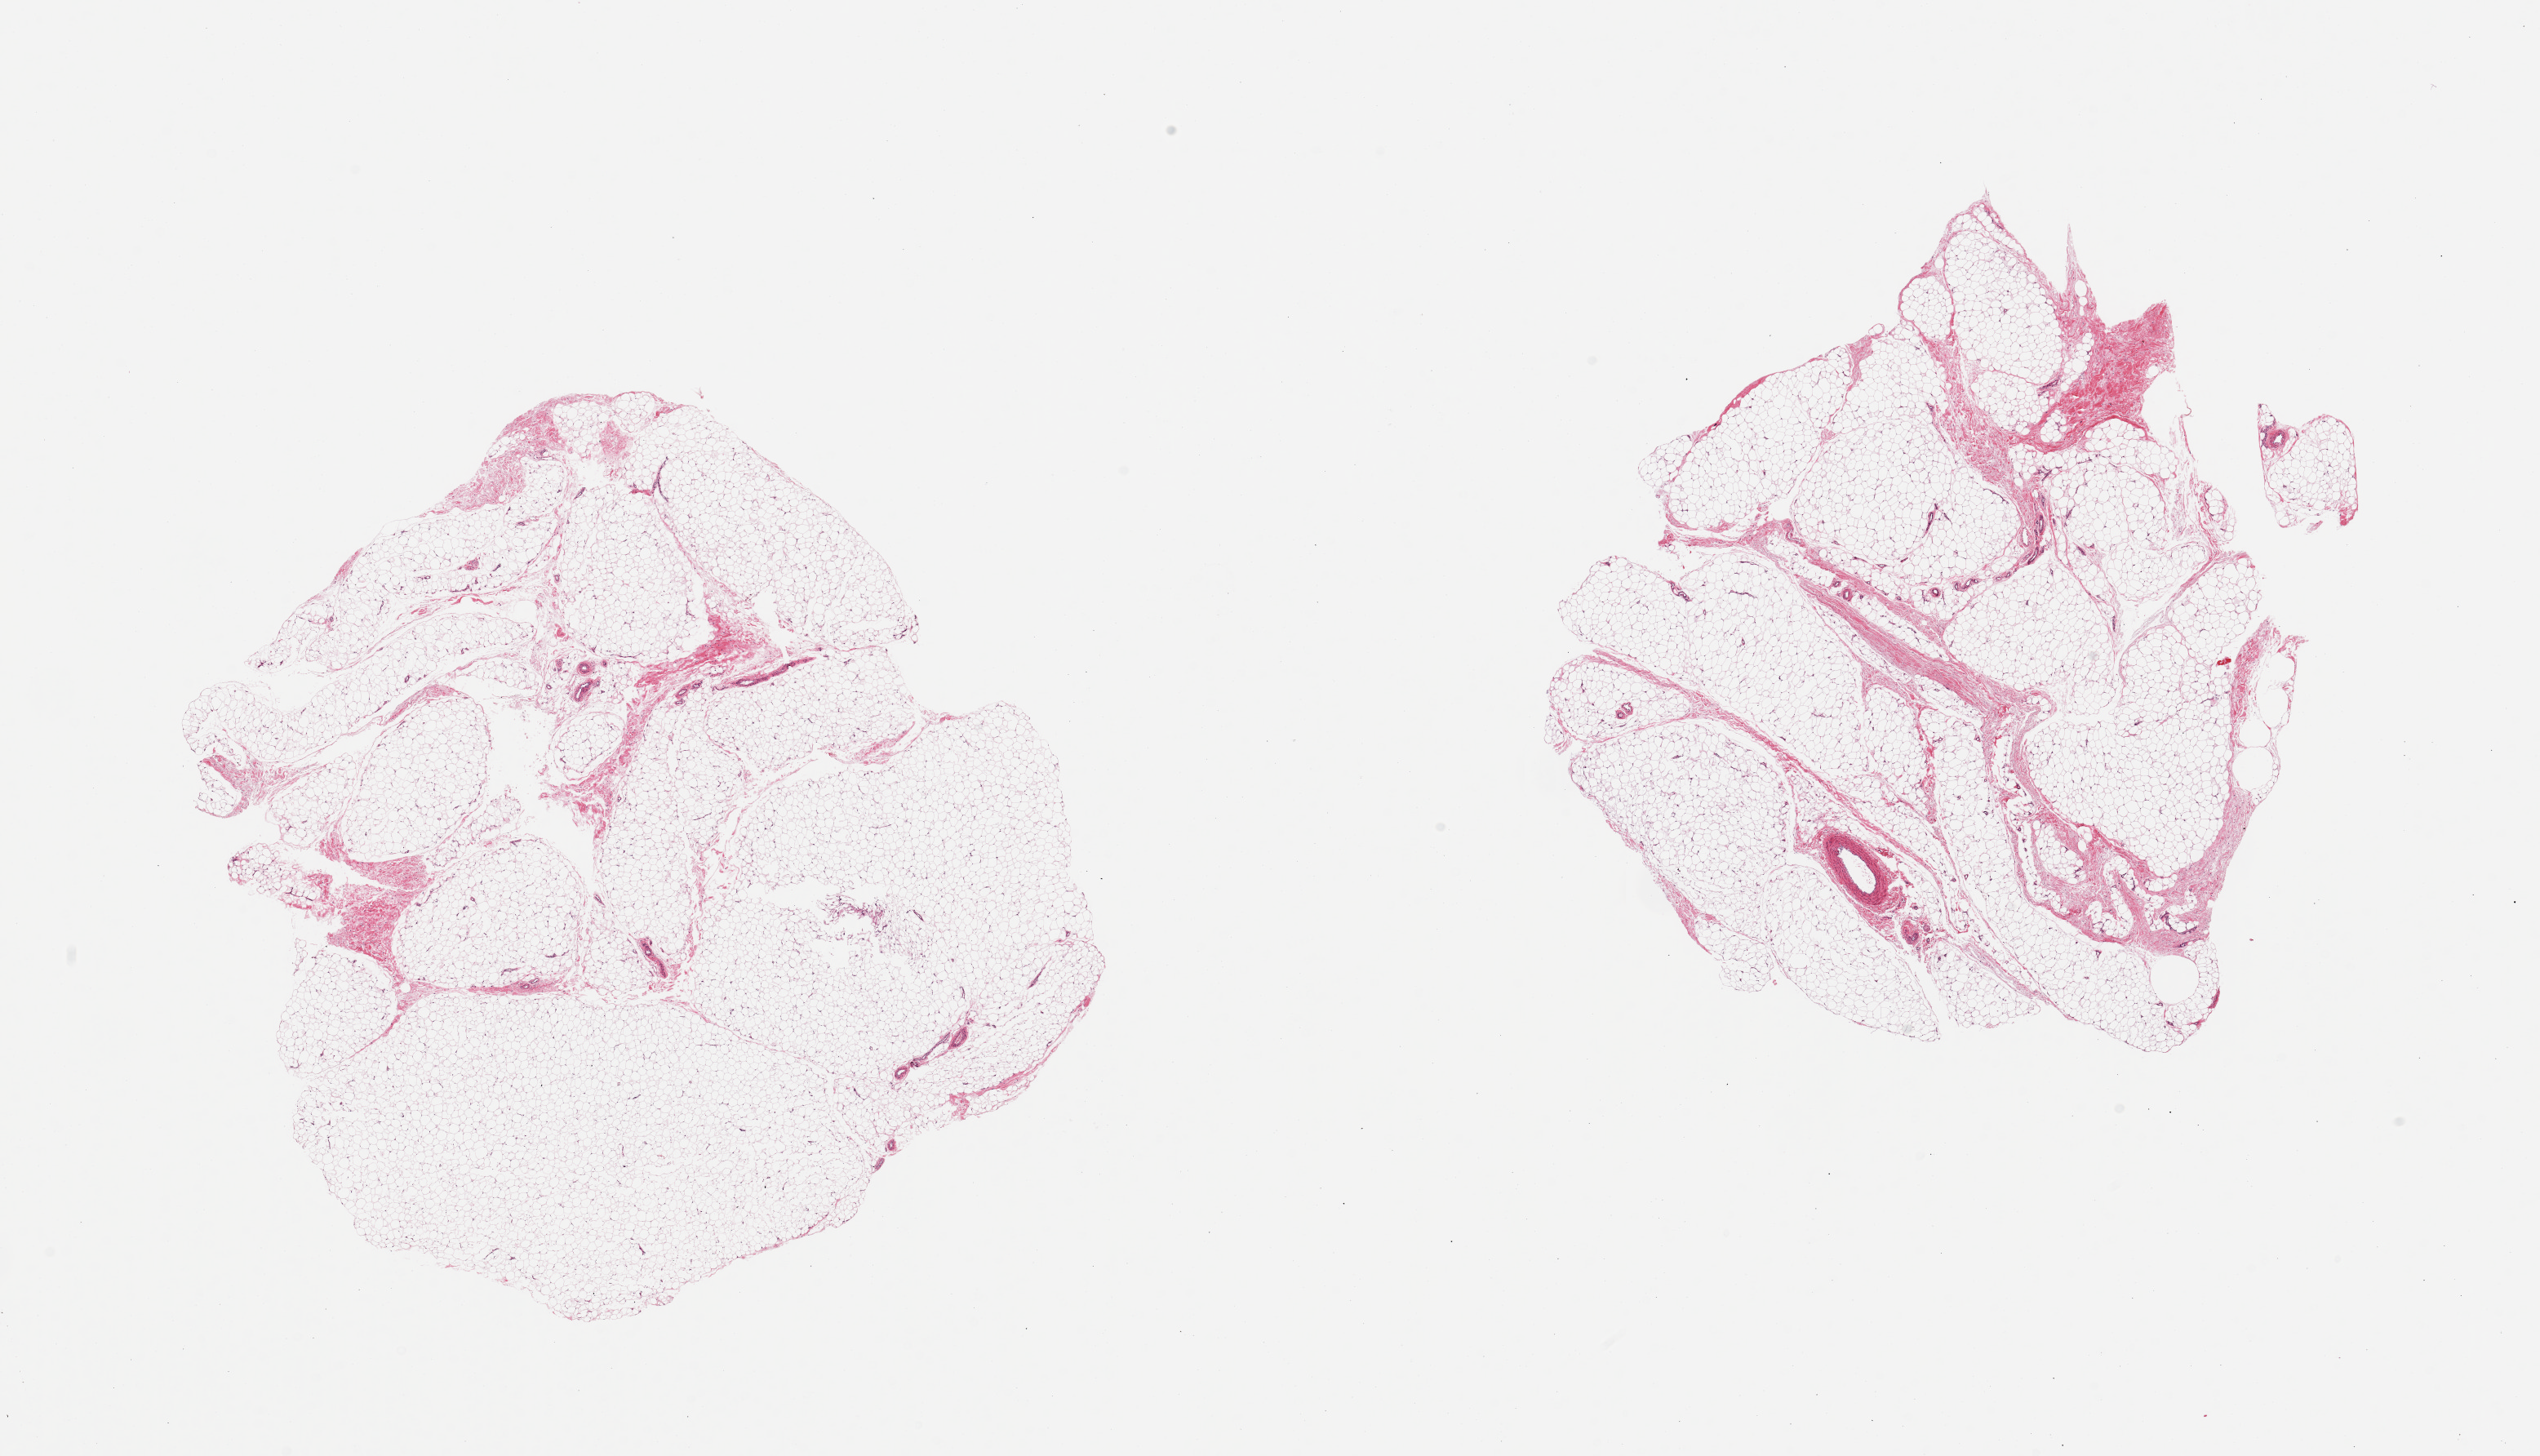
H&E whole-slide image — low-resolution overview of the scanned area, about 24.6 x 14.1 mm; PAXgene-fixed paraffin-embedded (PFPE) section; target tissue: adipose tissue; tissue donor sample. Female donor.
* pathologist's review note for this sample: 2 pieces; 5 & 10% fibrous content